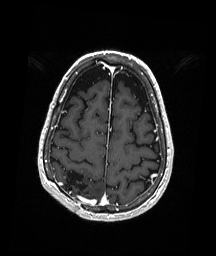
Brain MRI from a brain-tumour surgery series, one axial slice. T1-weighted post-contrast. 216 × 256 image matrix. From the clinical record (not read from this slice): histopathology: Astrocytoma; WHO grade: 3.
Annotated regions visible in this slice (manually delineated by an expert):
- previous resection cavity: bounding box (x1, y1, x2, y2) in pixels: (63, 171, 88, 196)